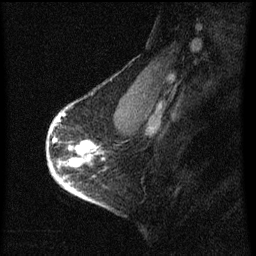
Breast MRI (dynamic contrast-enhanced), one sagittal slice; slice 46 of 60 in the series (ordered by position); dynamic contrast-enhanced series, image 2 of 3 at this slice position (ordered by acquisition); 1.5 T; TE 4.2 ms, TR 8 ms; 256 × 256 image matrix, field of view 180 × 180 mm. Female patient, age 56 years.
Annotated regions visible in this slice (semi-automatic segmentation, software-assisted and operator-edited):
- analysis volume of interest (the breast-tissue region the enhancement analysis was run in; not a lesion): bounding box [x1, y1, x2, y2] px = [50, 110, 105, 193]
- tumour enhancement mask (voxels above the 70 % enhancement threshold inside the analysis volume of interest): [52, 114, 97, 193]